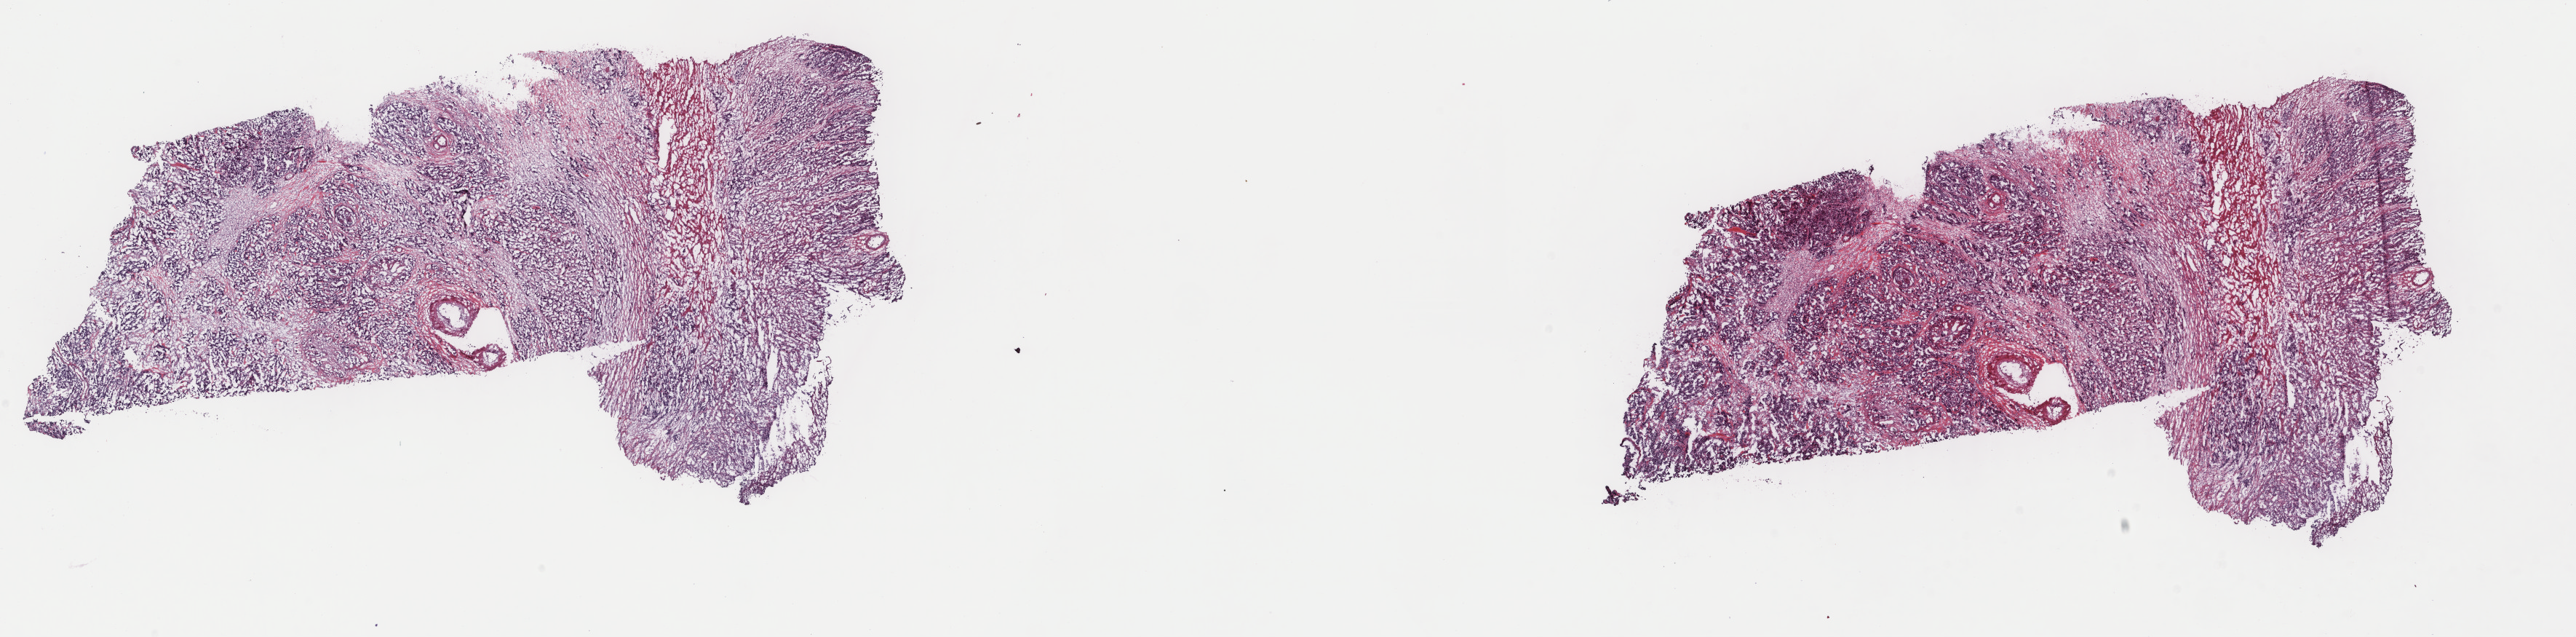
Digitized H&E tissue section (whole slide), shown as a low-resolution overview of the whole scanned area (about 28.1 x 6.9 mm, from a 40x scan), frozen section, sample: primary tumour, stomach. Patient: male, age at initial diagnosis 70 years. Histologic grade: G3 (poorly differentiated). Slide review estimates, as recorded: tumour cells 70%, tumour nuclei 70%, normal cells 0%, stromal cells 30%, necrosis 0%. Inflammatory infiltration, as recorded: lymphocyte infiltration 5%, monocyte infiltration 2%, neutrophil infiltration 1%.
- lymph nodes positive (case pathology): 10 of 15 examined
- AJCC pathologic stage: IIIB
- TNM: T3 N3a M0
- pathologic diagnosis: Adenocarcinoma, NOS (gastric antrum)